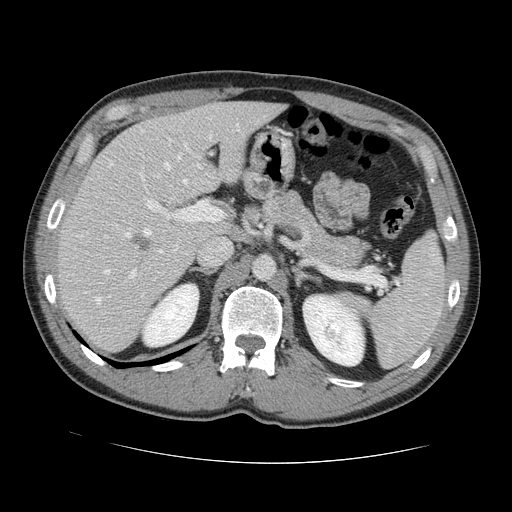
Contrast-enhanced abdominal CT, one axial slice. Position 84 of 131 along the scan axis. Intravenous contrast given. Soft-tissue window (W 400 / L 40 HU). 2.5 mm slice thickness. 512 × 512 image matrix, field of view 380 × 380 mm. Male patient, age 40 years. Case-level facts recorded for this patient, not image findings: diagnosis: colorectal cancer liver metastases, imaged before liver resection; multiple liver metastases: yes; largest metastasis: 2.9 cm; chemotherapy before resection: yes.
Outlined on this slice (manually delineated by an expert):
- hepatic veins: box from (x=95, y=153) to (x=187, y=304) px
- liver: (x=60, y=102)–(x=280, y=352)
- planned liver remnant (the part of the liver to remain after resection): (x=103, y=102)–(x=282, y=233)
- portal vein (with intrahepatic branches): (x=104, y=172)–(x=223, y=279)
- liver metastasis: (x=131, y=234)–(x=154, y=254)